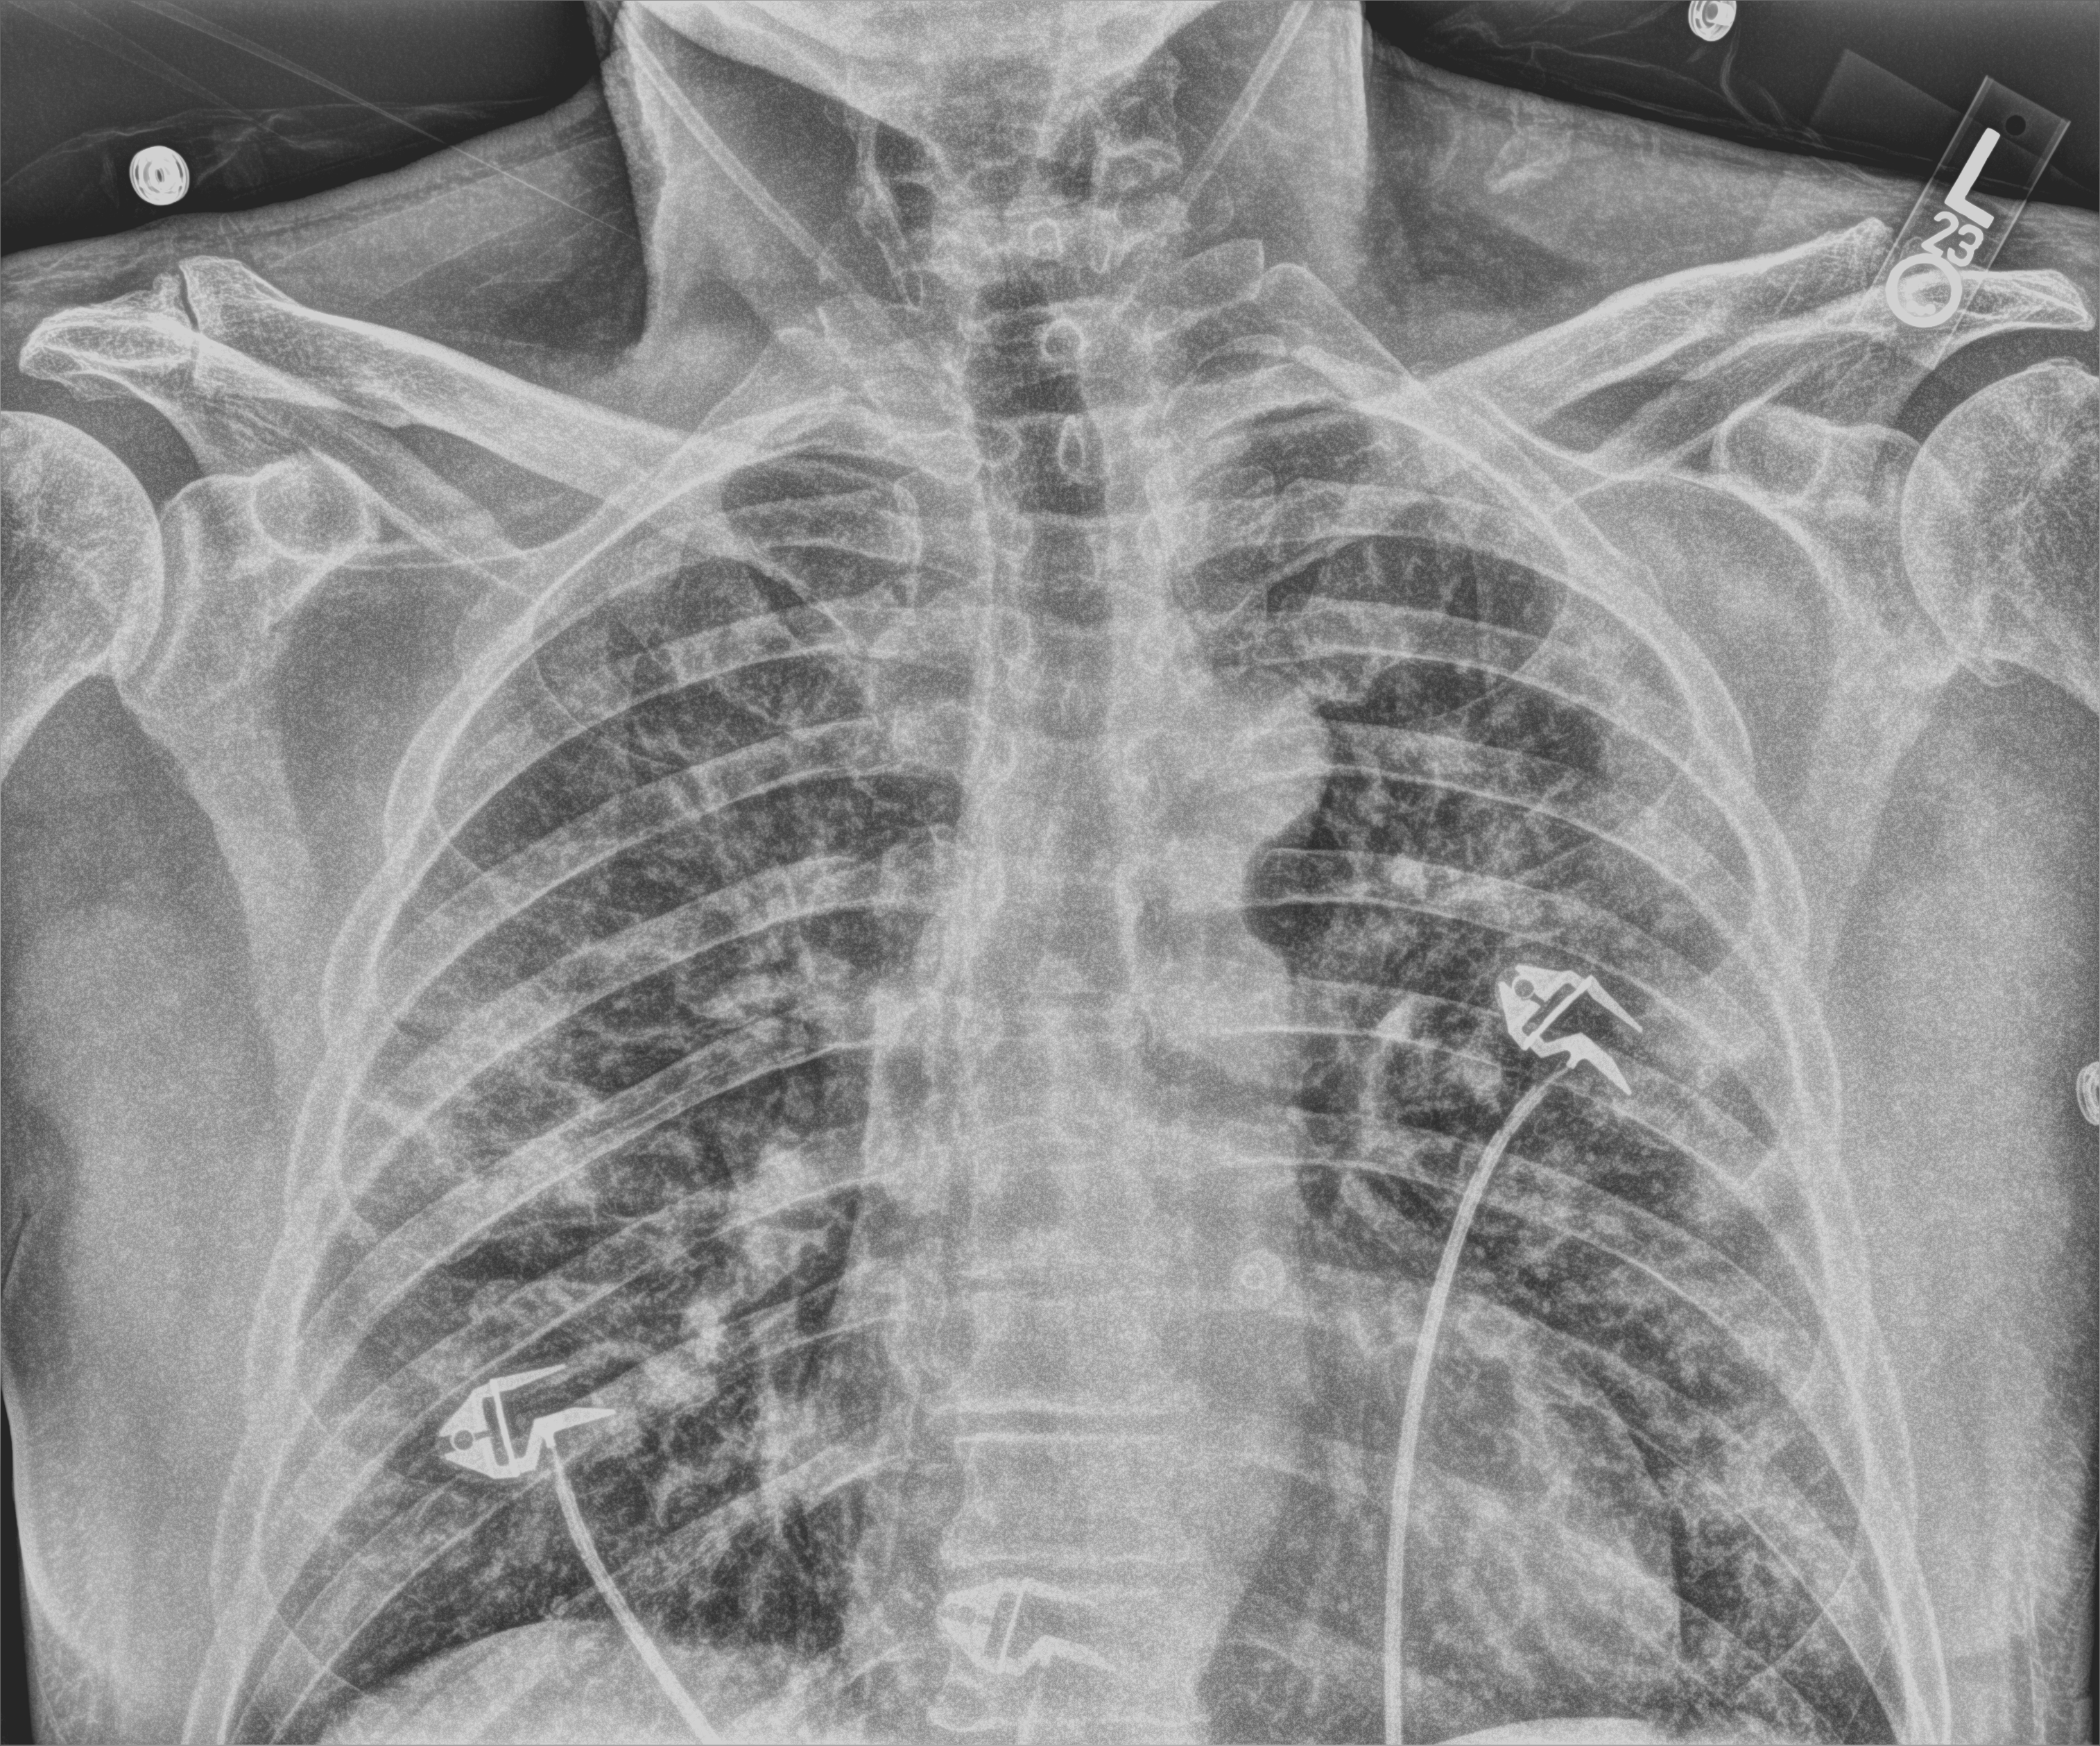
Portable chest radiograph. Male patient hospitalised with COVID-19, age 18–59 years.
From the hospital-stay record, not from the radiograph (when in the stay this image was taken is not recorded): length of hospital stay: 11 days; mechanically ventilated during this hospital stay: no.